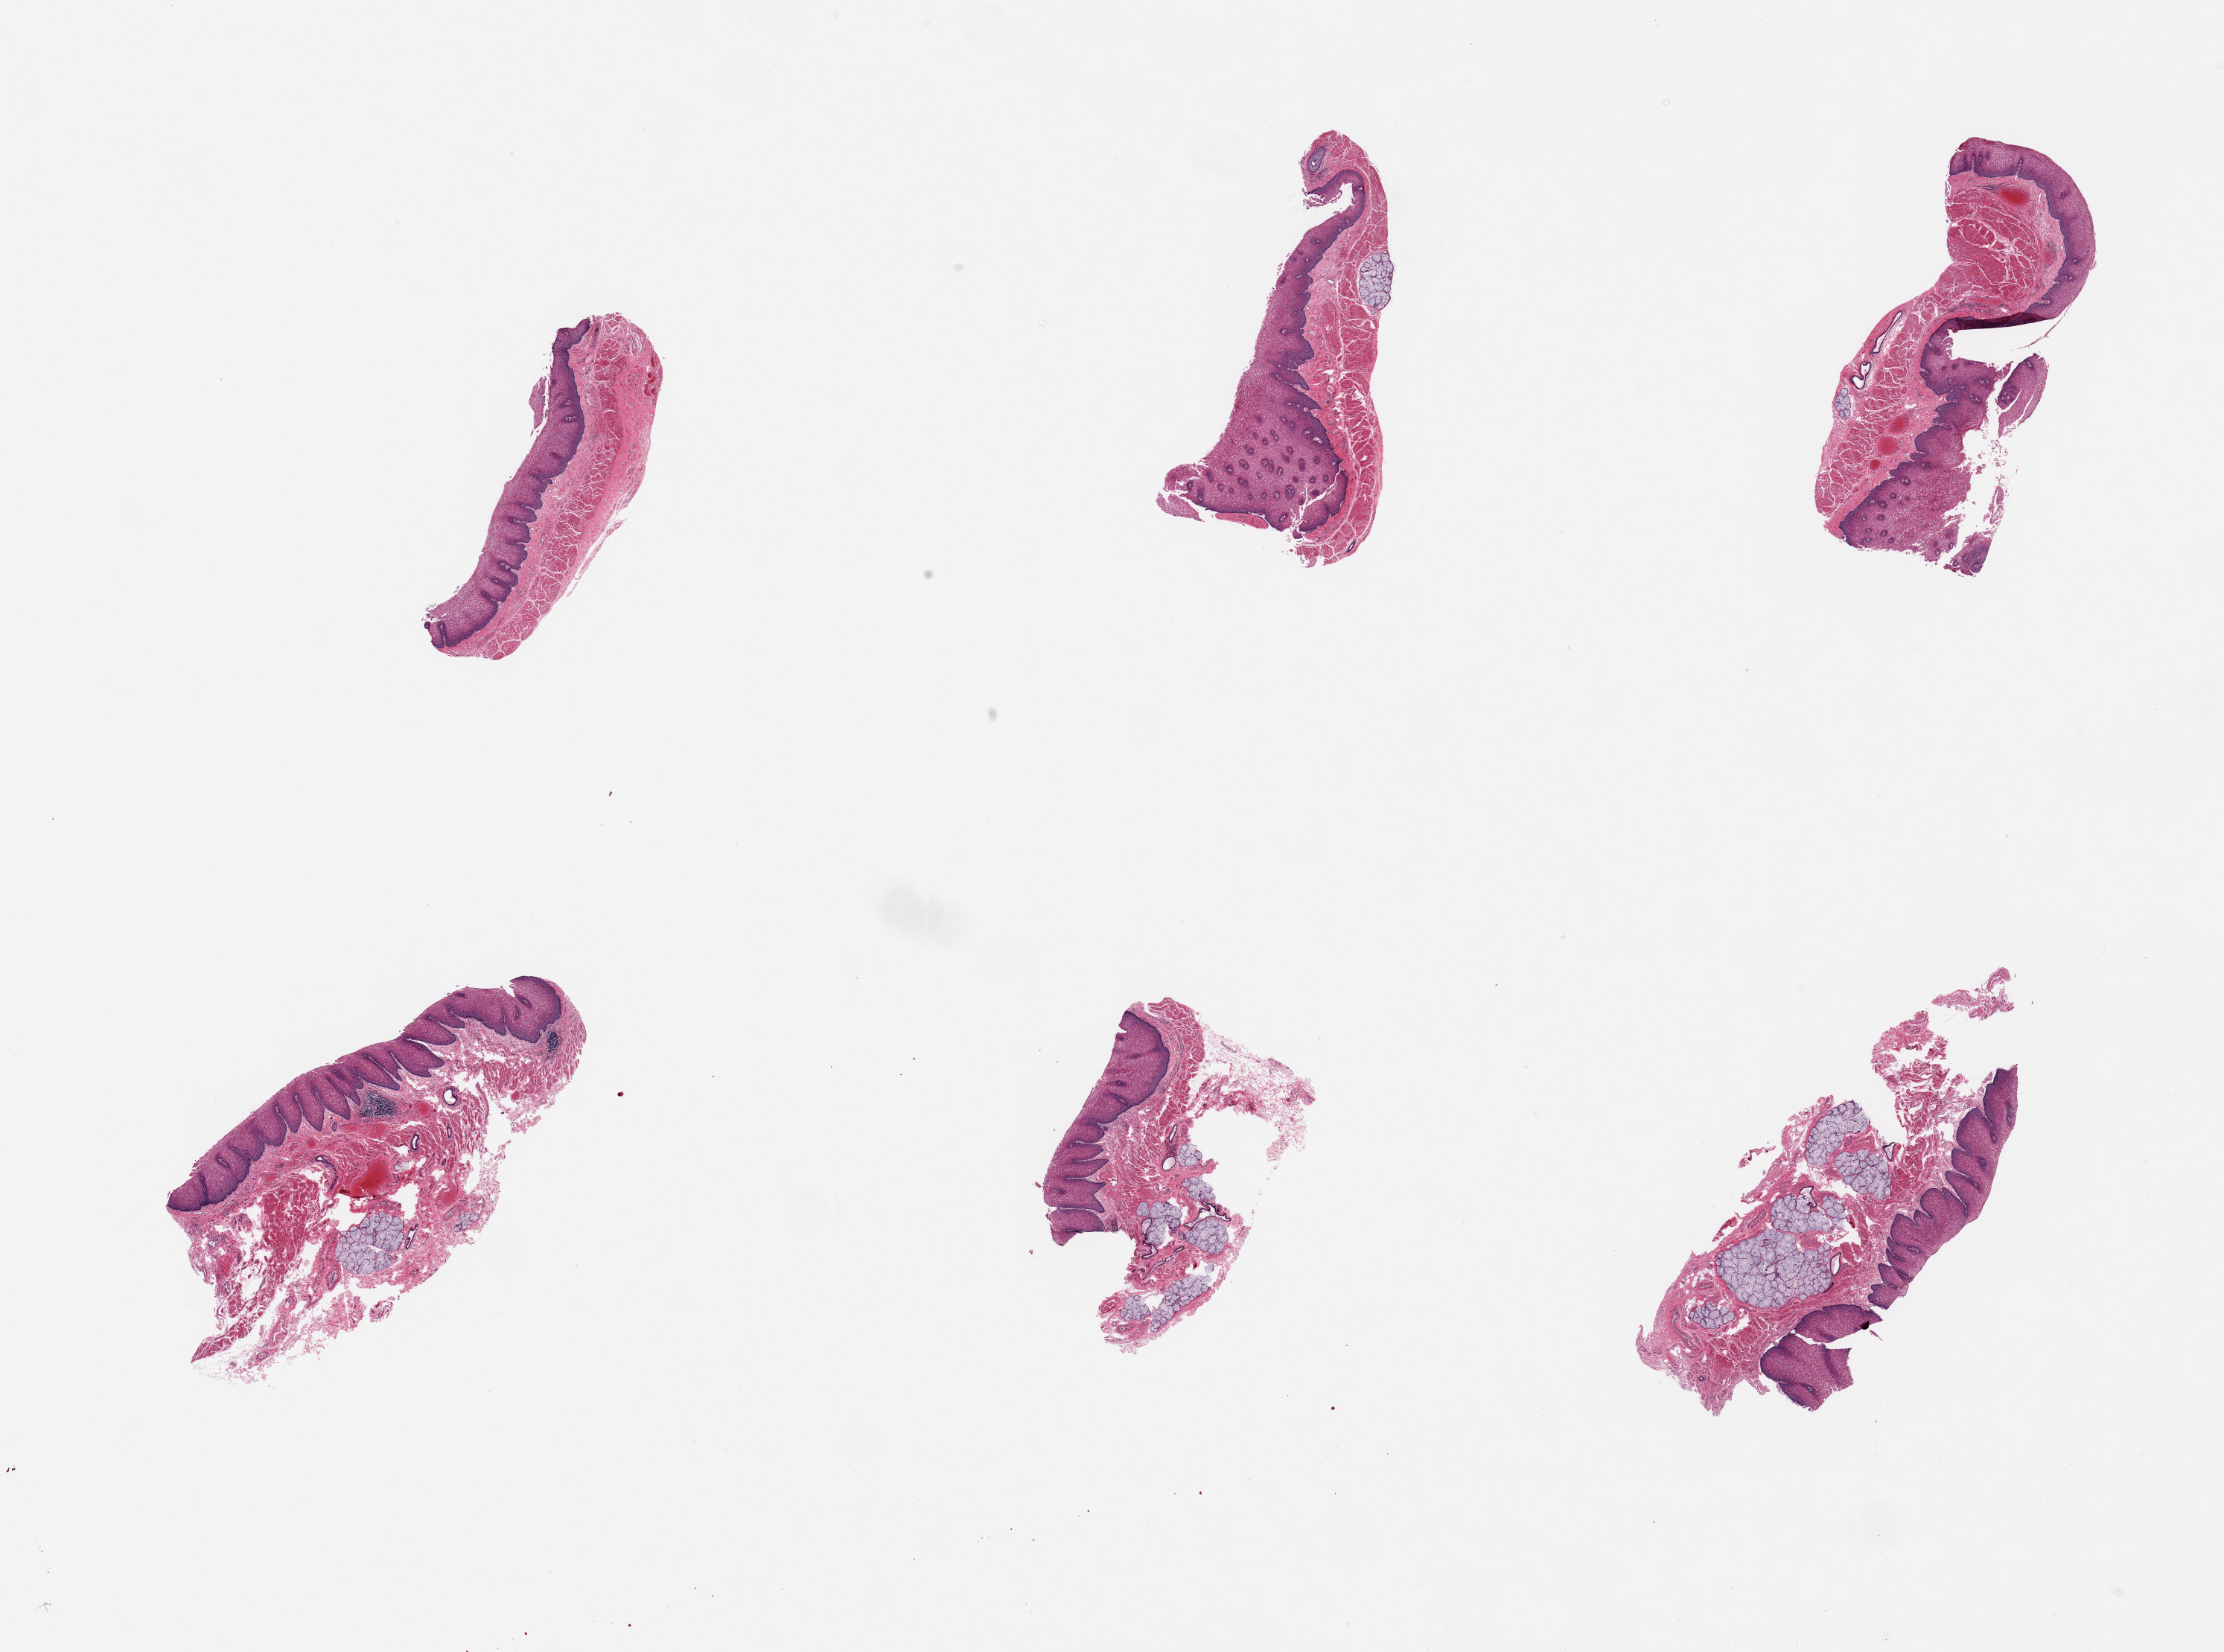
H&E whole-slide image, shown as a low-resolution overview of the whole scanned area (about 23.6 x 17.6 mm). PAXgene-fixed paraffin-embedded (PFPE) section. Target tissue: esophageal mucous membrane. Tissue donor sample. Donor sex: male.
Reviewer comment on this tissue sample: 6 pieces; squamous mucosa up to ~0.4mm, ~25% of thickness.